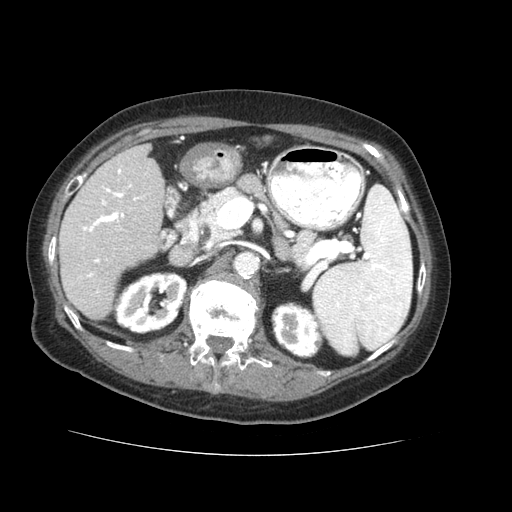
Contrast-enhanced abdominal CT (liver protocol), one axial slice. Slice 23 of 73 in the series (ordered by position). Reconstruction kernel STANDARD. 120 kVp. Soft-tissue window (W 400 / L 40 HU). 2.5 mm slice thickness. 512 × 512 image matrix, field of view 360 × 360 mm. Case-level facts recorded for this patient, not image findings: diagnosis: hepatocellular carcinoma (patient treated with transarterial chemoembolisation; whether this scan precedes or follows treatment is not stated here); TNM stage (as recorded): Stage-IVB; Child-Pugh class: A; tumour differentiation: well differentiated.
Structures marked on this image (semi-automatic segmentation, software-assisted and operator-edited):
- liver parenchyma outside the tumour (the mass and vessels are separate outlines, so this box may not span the whole liver): bounding box <58,144,164,318> (left, top, right, bottom; pixels)
- liver vessels: <78,168,149,294>